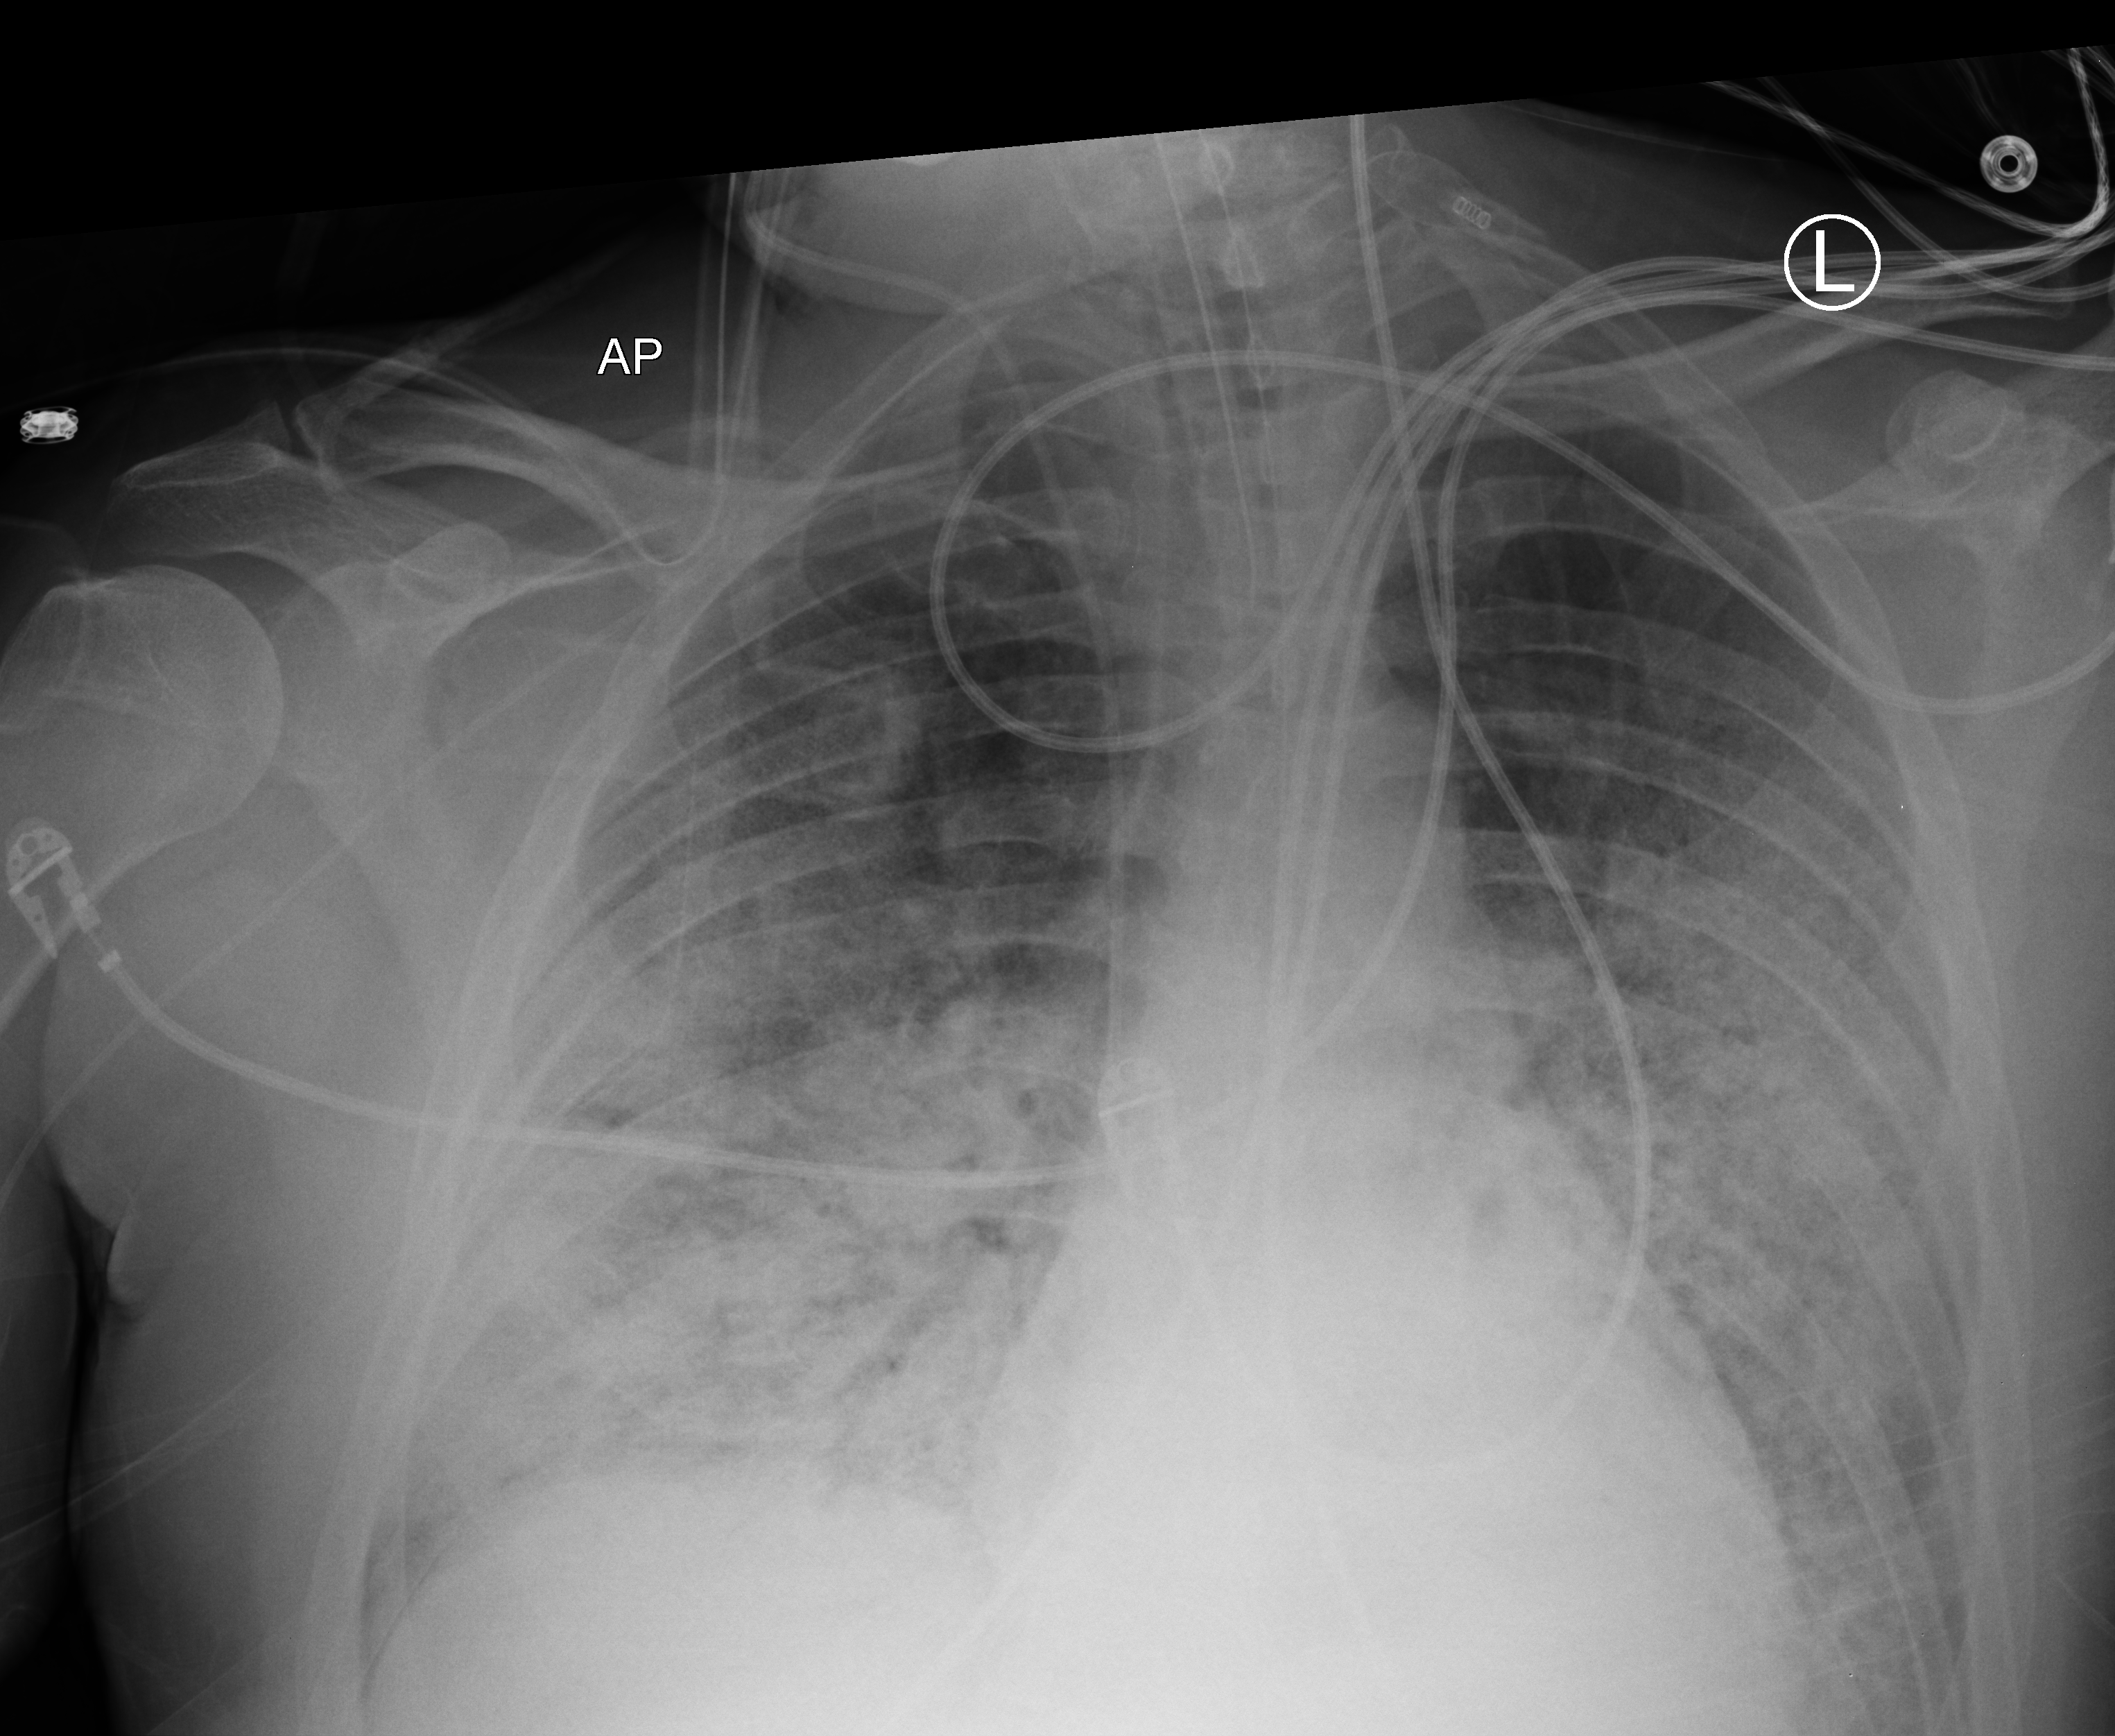
Chest X-ray (portable), anteroposterior (AP) projection. Male patient hospitalised with COVID-19, age 18–59 years.
Hospital-stay facts (about this admission, not read from this image; timing relative to this image not recorded): admitted to intensive care during this hospital stay: yes; mechanically ventilated during this hospital stay: yes; COPD (admission record): no.